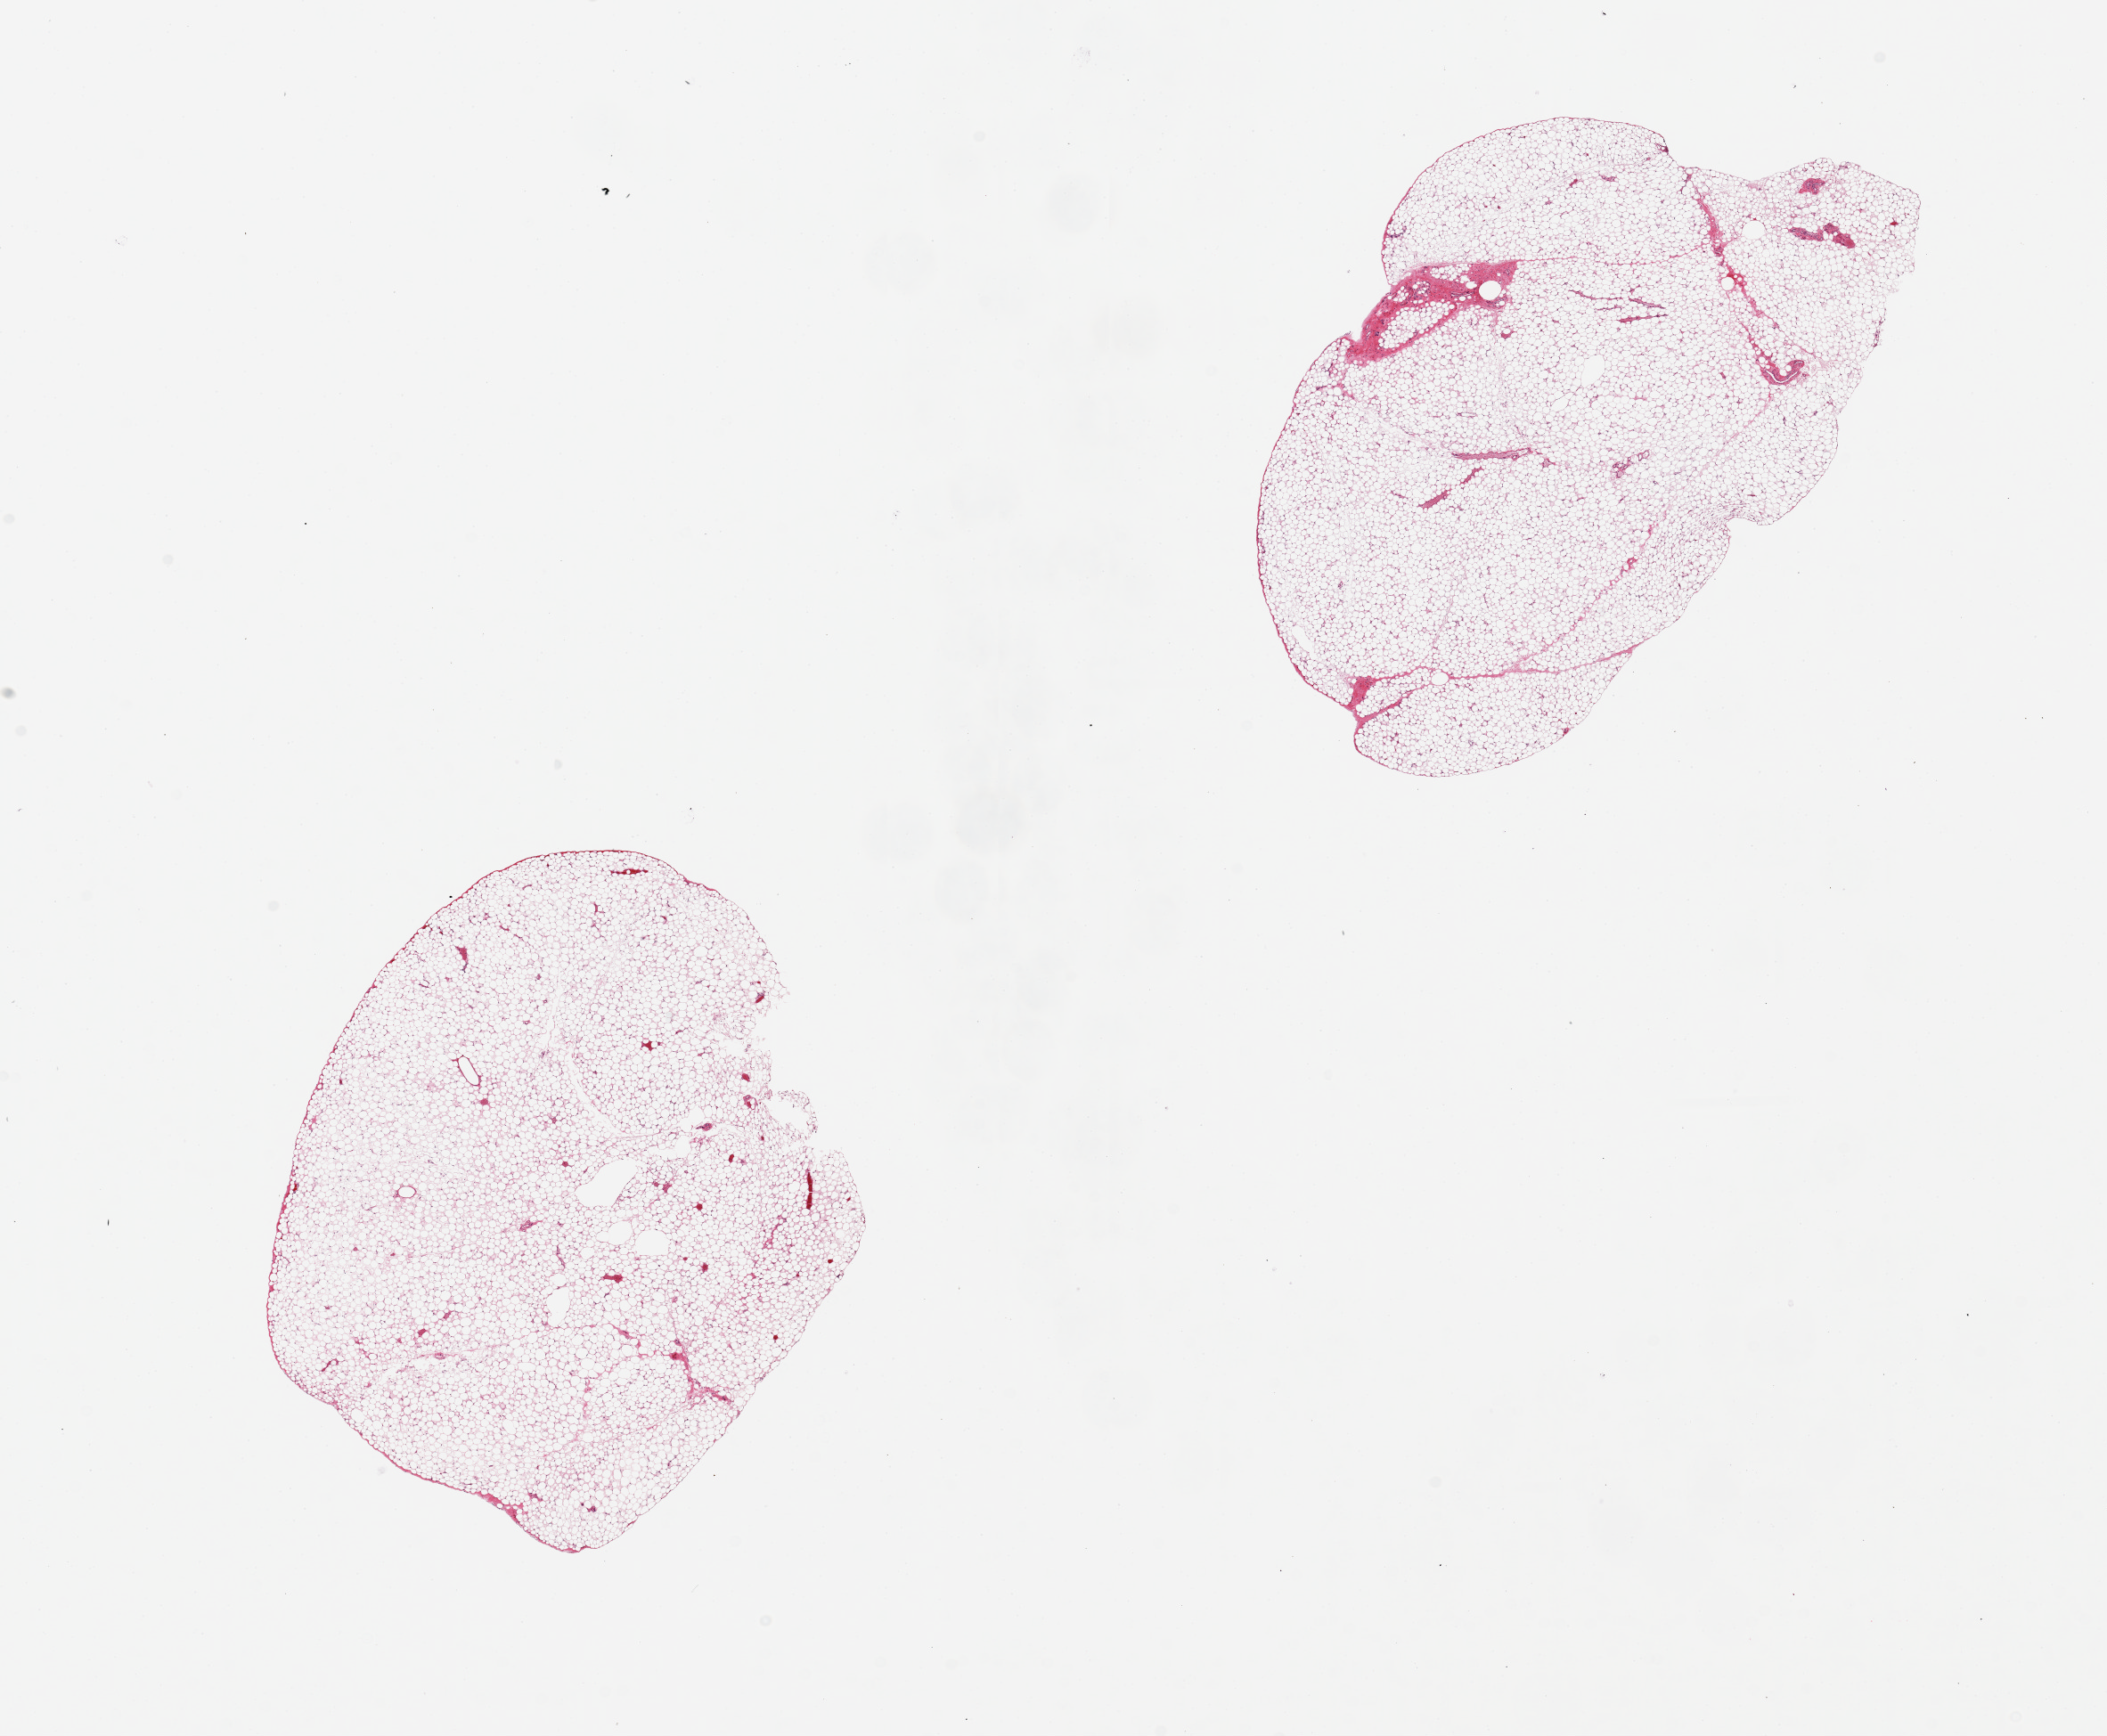
Digitized hematoxylin and eosin (H&E)-stained section, brightfield, low-resolution overview of the scanned area, about 18.7 x 15.4 mm. PAXgene-fixed paraffin-embedded (PFPE) section. Target tissue: omentum. Tissue donor sample. Donor: male.
Review note (as recorded): 2 pieces, 6x5 & 7x4mm; no artifacts.